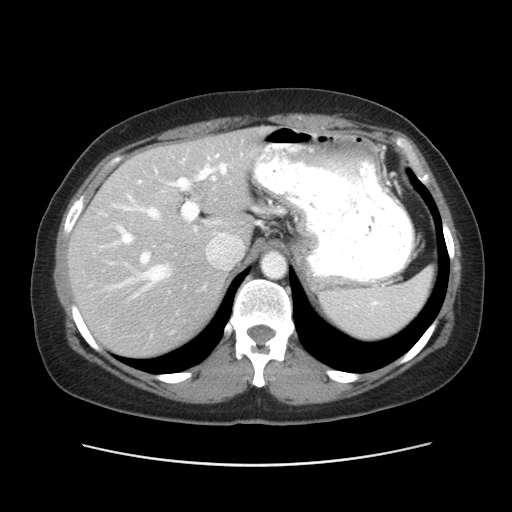
Contrast-enhanced abdominal CT, one axial slice; slice 37 of 52 in the series (ordered by position); soft-tissue window (W 400 / L 40 HU); 5 mm slice thickness; 512 × 512 image matrix, field of view 362 × 362 mm. Female patient, age 48 years. Case-level facts recorded for this patient, not image findings: diagnosis: colorectal cancer liver metastases, imaged before liver resection; multiple liver metastases: yes; largest metastasis: 4.5 cm; disease in both lobes: yes.
Structures marked on this image (outlined manually by an expert reader):
- hepatic veins: bounding box <107,158,226,297> (left, top, right, bottom; pixels)
- liver: <70,130,261,357>
- planned liver remnant (the part of the liver to remain after resection): <142,130,260,239>
- portal vein (with intrahepatic branches): <97,159,215,267>